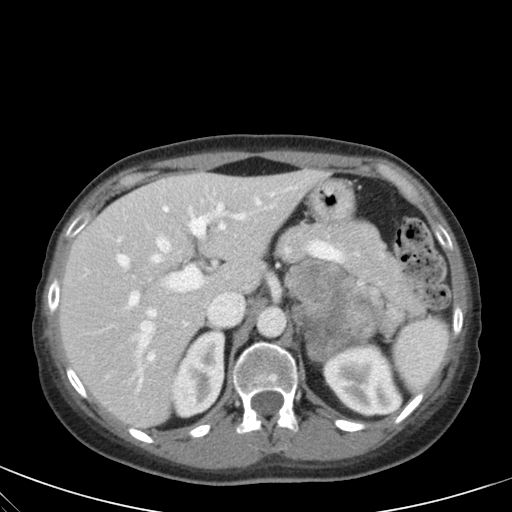
Contrast-enhanced abdominal CT, one axial slice. Position 39 of 59 along the scan axis. 120 kVp. Soft-tissue window (W 400 / L 40 HU). 512 × 512 image matrix, field of view 350 × 350 mm. Female patient, age 28 years. Case-level facts recorded for this patient, not image findings: diagnosis: adrenocortical carcinoma; tumour side: left adrenal; tumour size at pathology: 7 cm; Ki-67 index: 40 %; stage (as recorded): 4.
Structures marked on this image (semi-automatically segmented with operator editing):
- mass: bounding box [x1, y1, x2, y2] px = [287, 262, 403, 360]